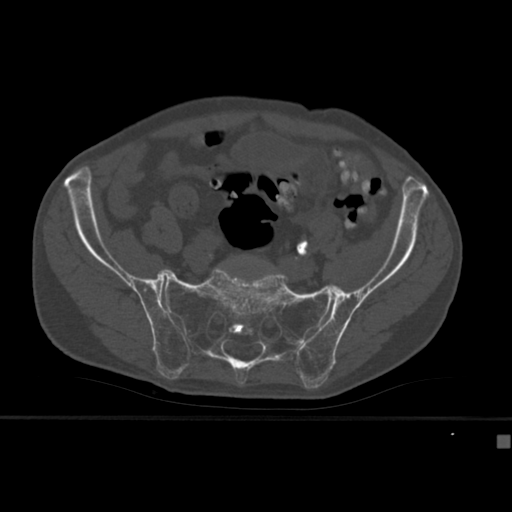
CT including the spine, one axial slice. Position 65 of 430 along the scan axis. 120 kVp. Bone window (W 1800 / L 400 HU). 1.5 mm slice thickness. 512 × 512 image matrix, field of view 337 × 337 mm. Male patient, age 64 years. From the clinical record (not read from this slice): primary cancer: uterus.
Outlined on this slice (semi-automatic segmentation, software-assisted and operator-edited):
- L5 vertebra: bounding box (x1, y1, x2, y2) in pixels: (241, 254, 276, 270)